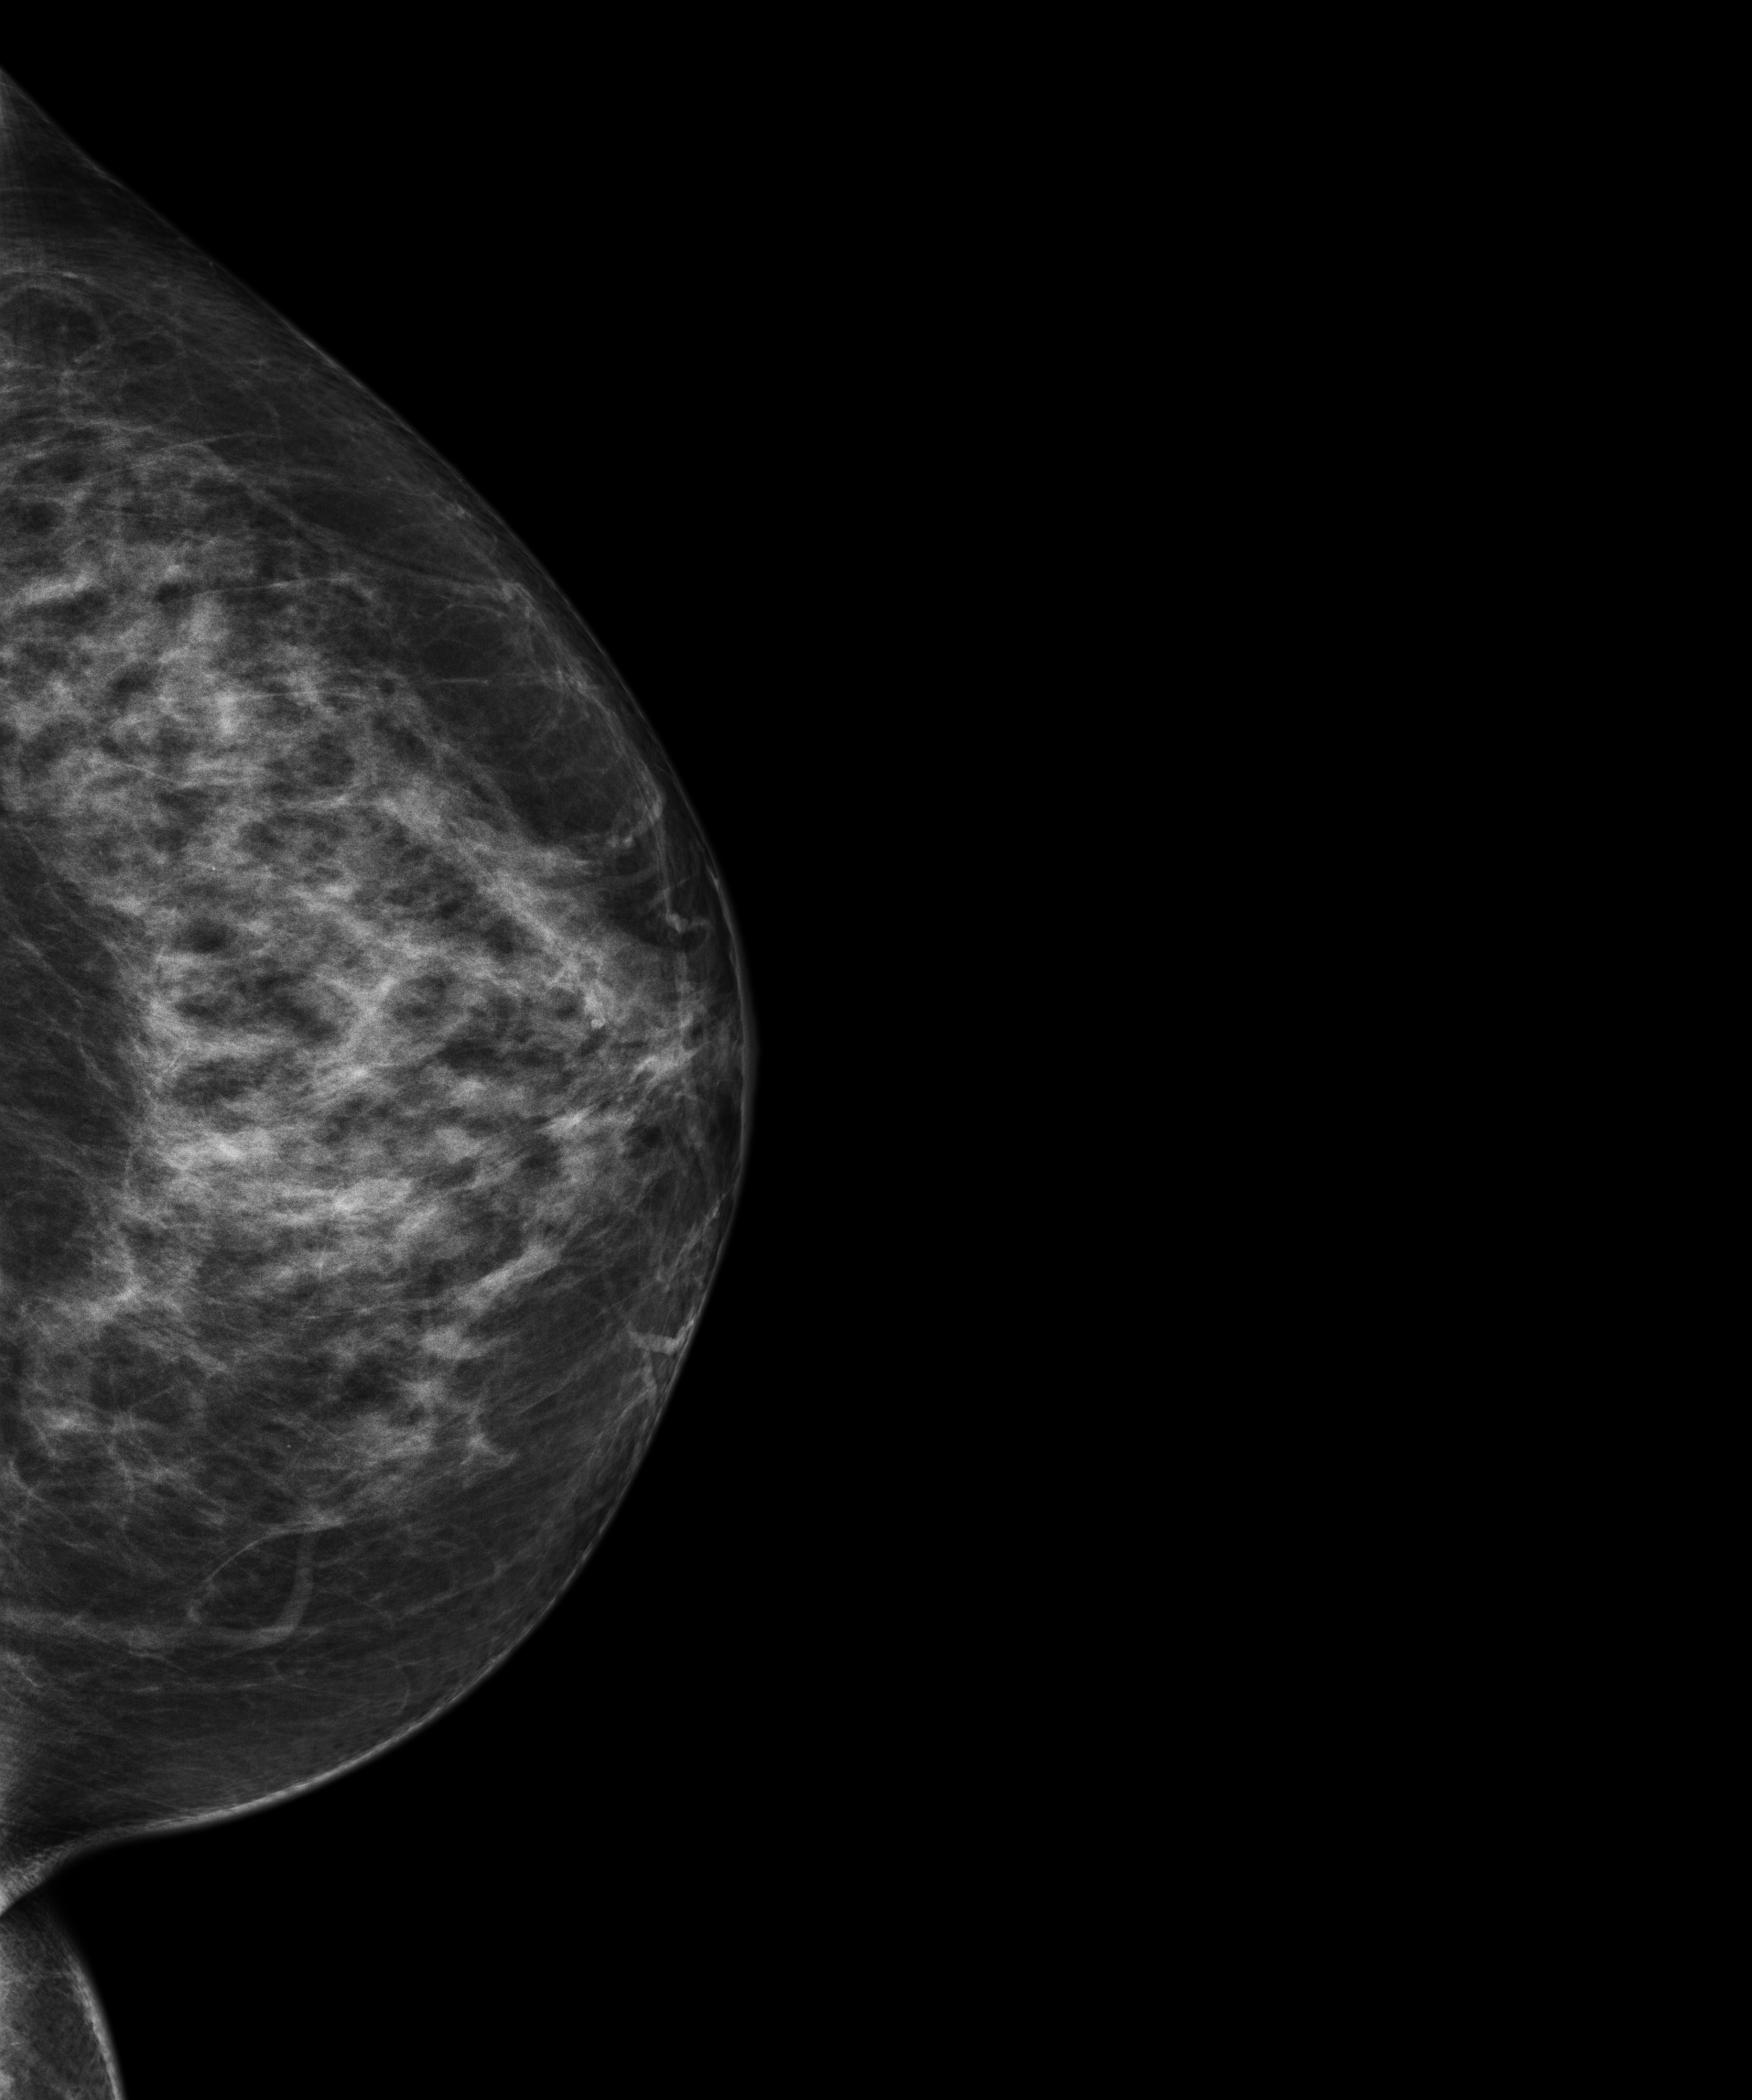
Digital mammogram (FFDM), left breast, craniocaudal (CC) view, screening examination, compressed breast thickness 63 mm. Female patient, age 58 years.
Breast density at the screening exam (both breasts): heterogeneously dense (BI-RADS density category c). Final BI-RADS assessment for this screening round (tomosynthesis exam, both breasts): category 1. Recall: no recall after this screen.